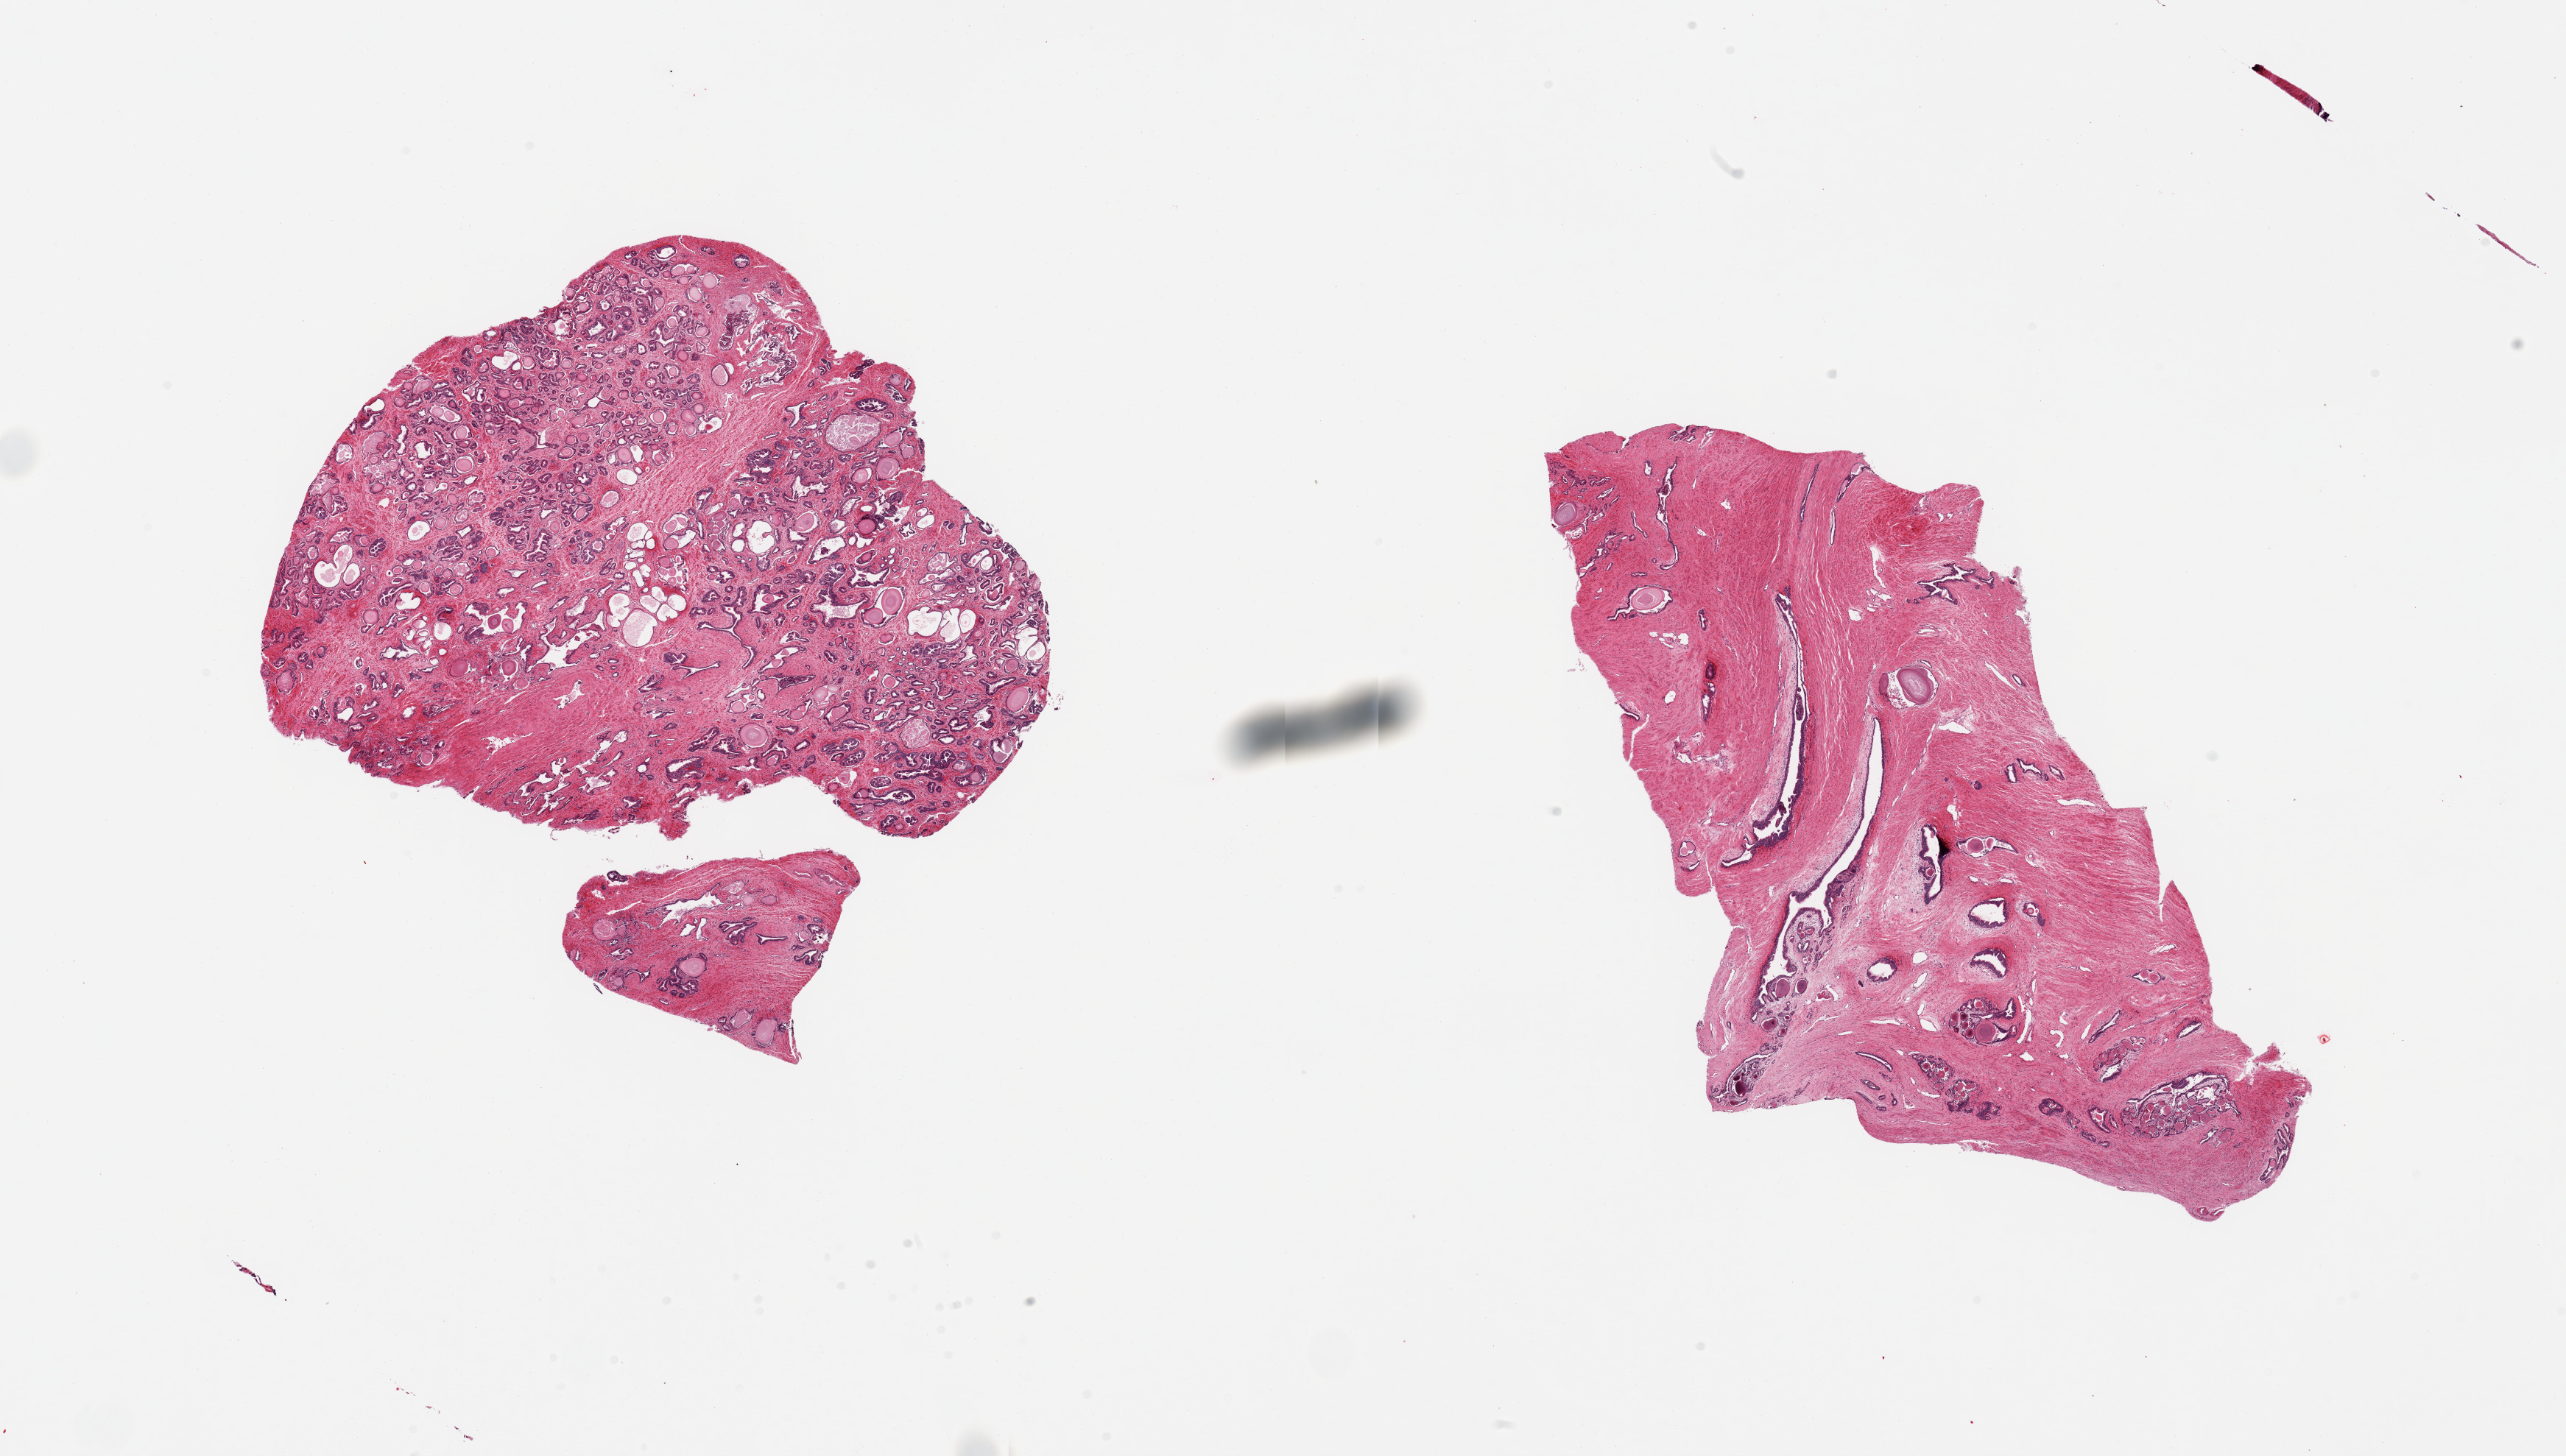
Whole-slide image, haematoxylin and eosin stain, brightfield — whole scanned area (about 27.6 x 15.6 mm, acquisition: 20x scan) shown as a low-resolution overview; PAXgene-fixed, paraffin-embedded tissue; section of prostate (target tissue); tissue donor sample. Donor: male.
Review note (as recorded): 2 pieces.